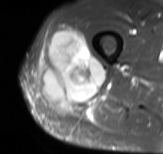
MRI of an extremity soft-tissue mass, one axial slice. Slice 37 of 61 in the series (ordered by position). STIR. MR volume resampled by the dataset authors to the PET/CT grid (not the native acquisition matrix). 3.27 mm slice thickness. 163 × 154 image matrix, field of view 159 × 150 mm. Male patient. From the clinical record (not read from this slice): histological type: poorly differentiated synovial sarcoma; grade: high; site of the primary tumour: right buttock.
Outlined on this slice (expert contour drawn on MRI and transferred to this co-registered scan by the dataset authors):
- gross tumour volume including surrounding oedema: box from (x=41, y=29) to (x=104, y=111) px
- gross tumour volume (mass): (x=41, y=30)–(x=104, y=111)